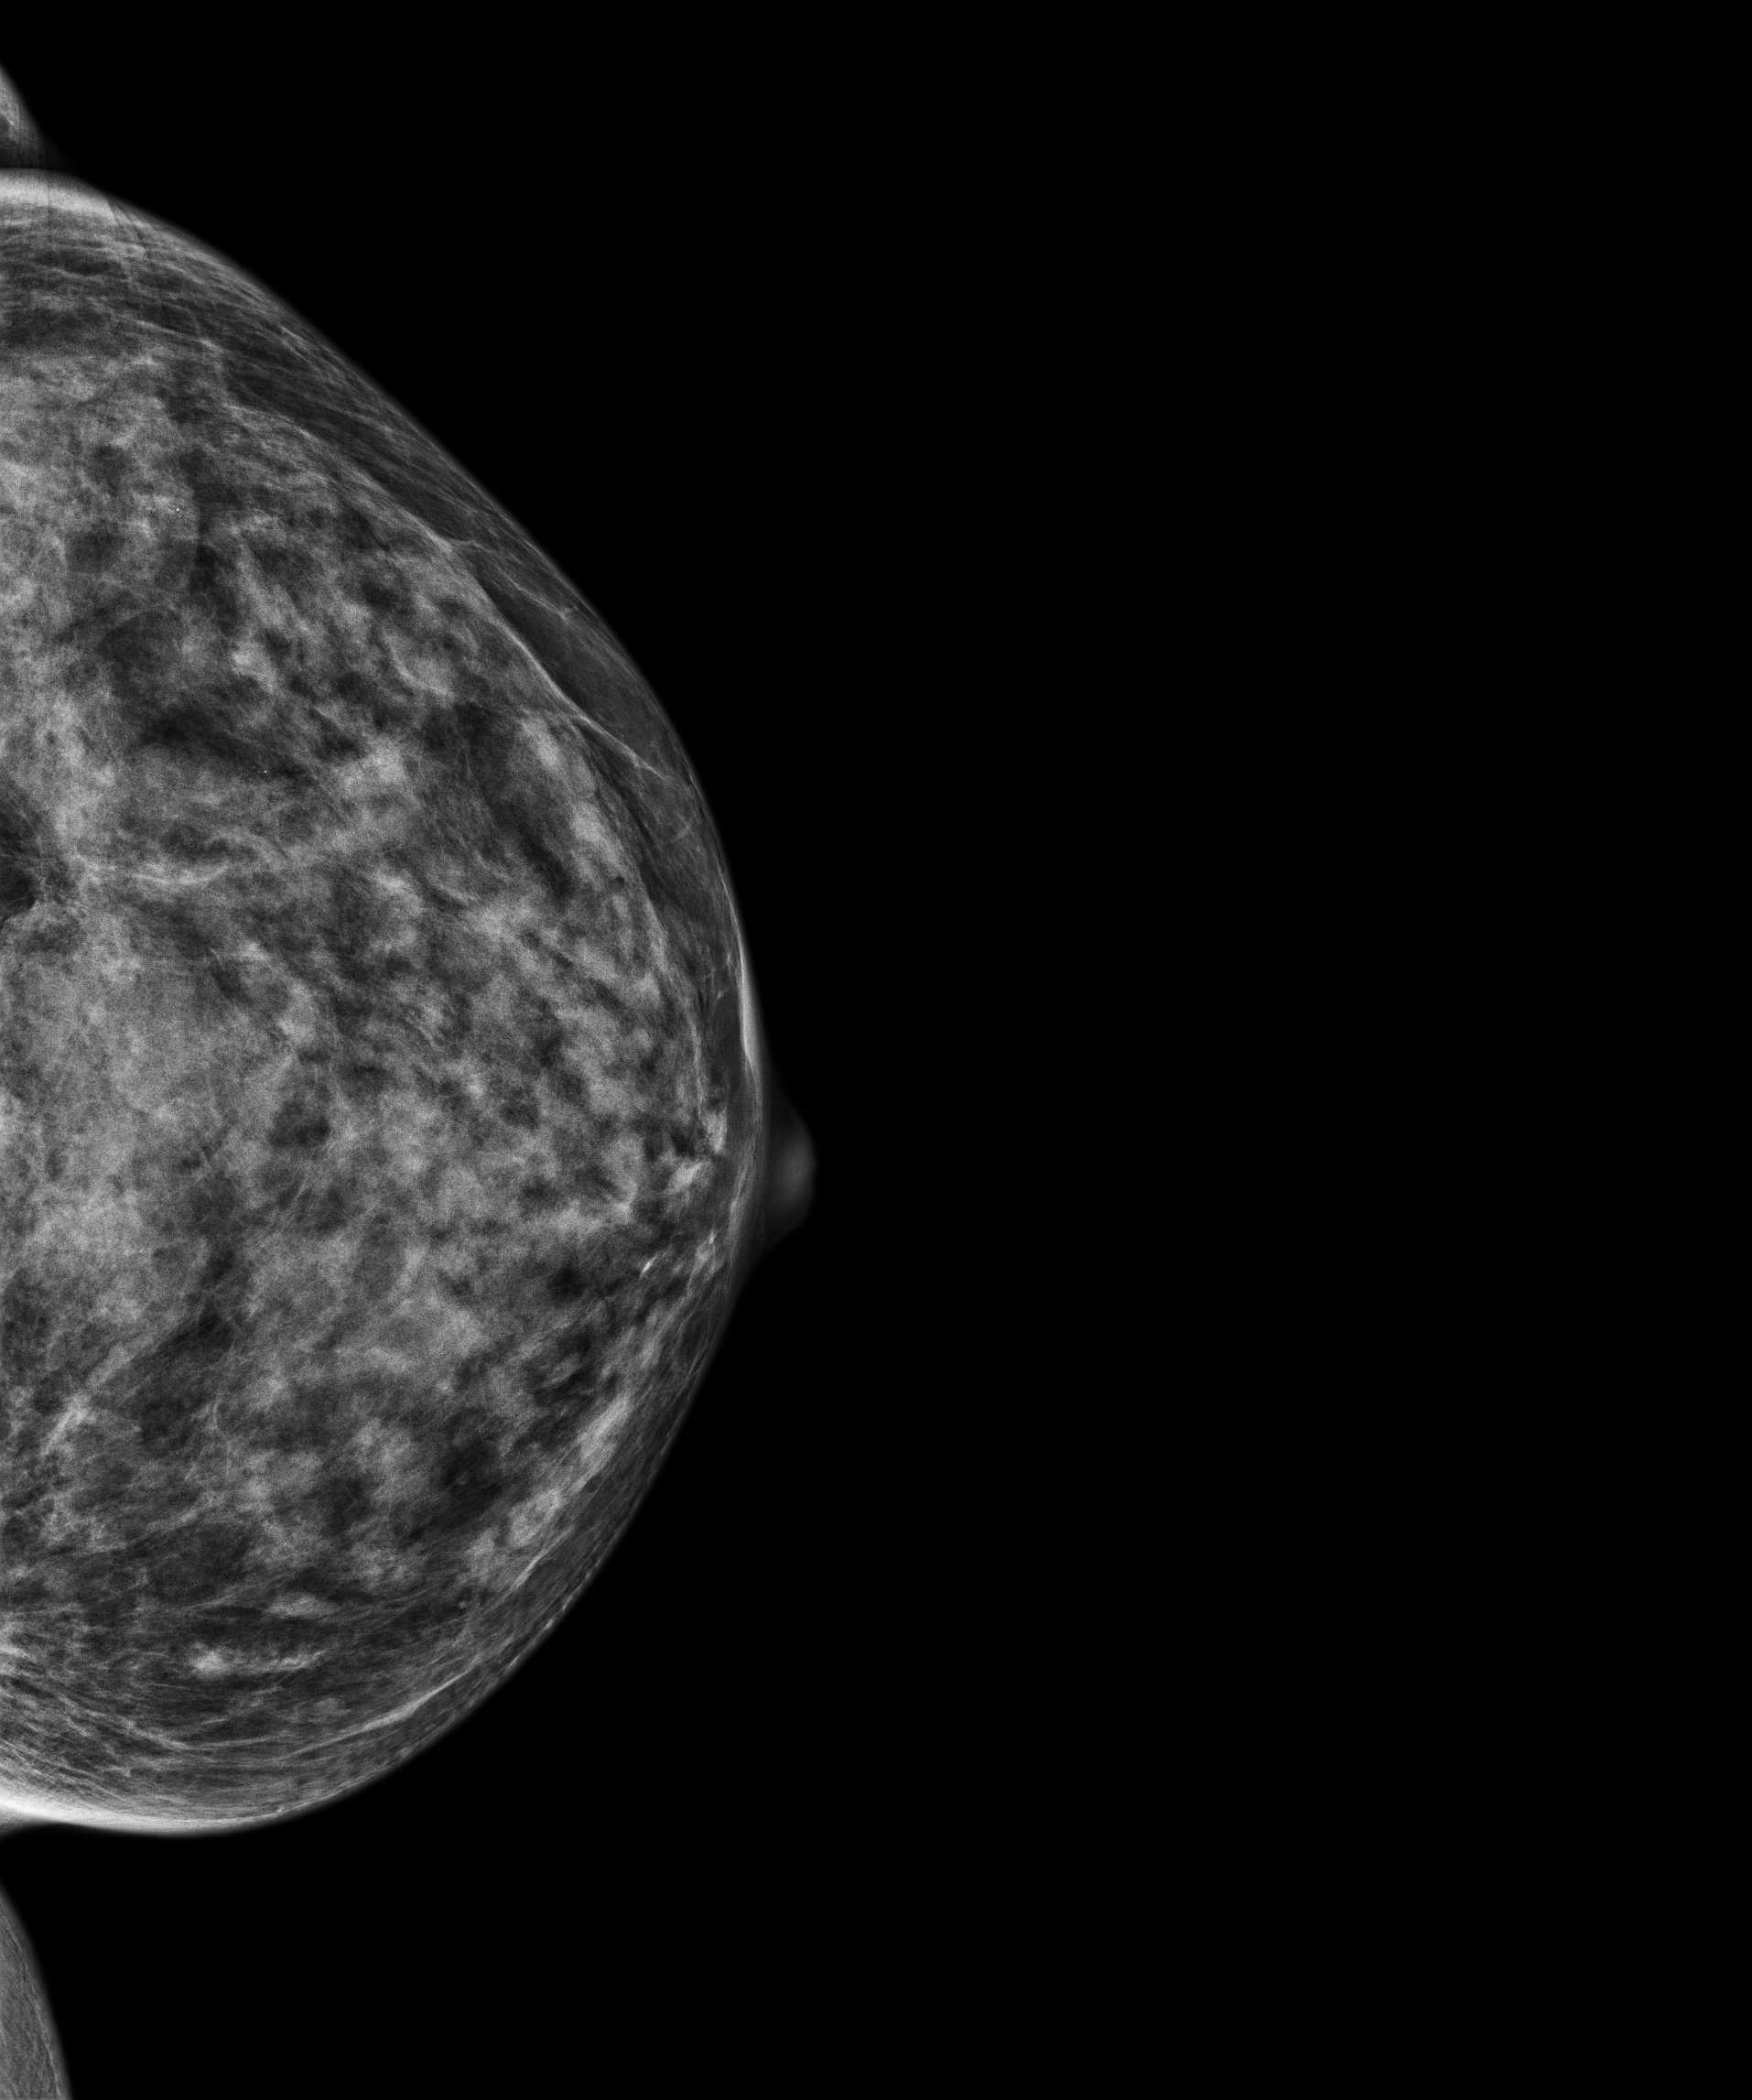
Screening examination, compressed breast thickness 35.3 mm, system: Senographe Pristina. Patient aged 74 years (female).
Image type: full-field digital mammogram. Breast: left. Projection: craniocaudal (CC) view.